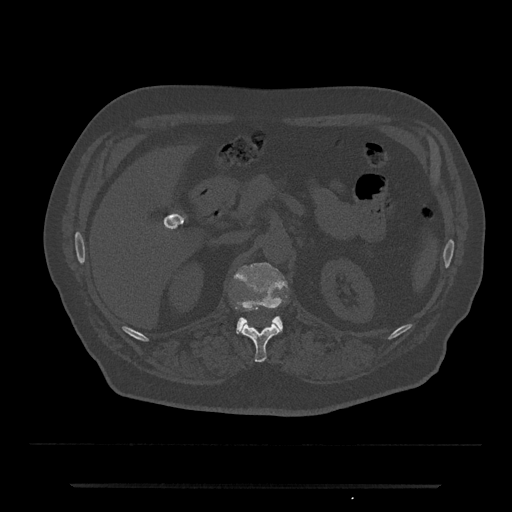
CT including the spine, one axial slice; slice 568 of 797 in the series (ordered by position); 120 kVp; bone window (W 1800 / L 400 HU); 512 × 512 image matrix, field of view 434 × 434 mm. Patient: male, 80 years. From the clinical record (not read from this slice): primary cancer: prostate.
Annotated regions visible in this slice (semi-automatically segmented with operator editing):
- L1 vertebra: bounding box <233,263,288,334> (left, top, right, bottom; pixels)
- T12 vertebra: <242,324,281,363>